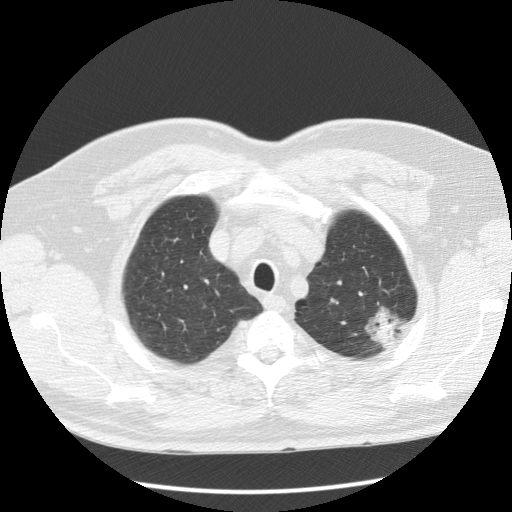
Low-dose screening chest CT, one axial slice; position 105 of 123 along the scan axis; reconstruction kernel STANDARD; lung window (W 1500 / L -600 HU); 2.5 mm slice thickness; 512 × 512 image matrix, field of view 355 × 355 mm.
Annotated regions visible in this slice (outlined manually by an expert reader):
- lesion 1 (tumor, upper lobe of left lung): bounding box (x1, y1, x2, y2) in pixels: (371, 314, 396, 343)